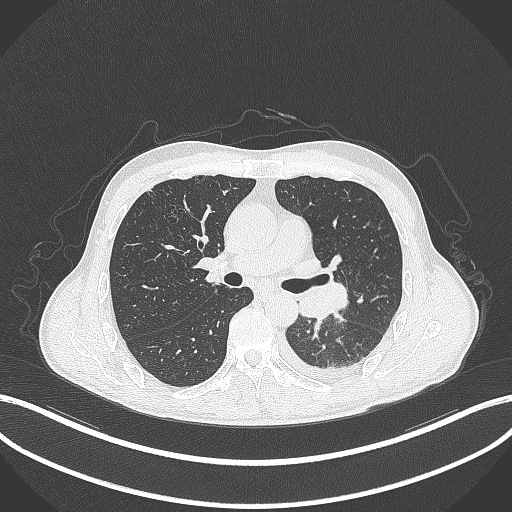
Chest CT, one axial slice. Slice 191 of 295 in the series (ordered by position). Reconstruction kernel B70f. Lung window (W 1500 / L -600 HU). 1 mm slice thickness. 512 × 512 image matrix. Male patient, age 47 years. Case-level facts recorded for this patient, not image findings: clinical TNM (as recorded): T3 N1 M1c.
Outlined on this slice (bounding box drawn by a radiologist):
- lung tumour (recorded histology: small cell carcinoma): bounding box <295,280,352,322> (left, top, right, bottom; pixels)